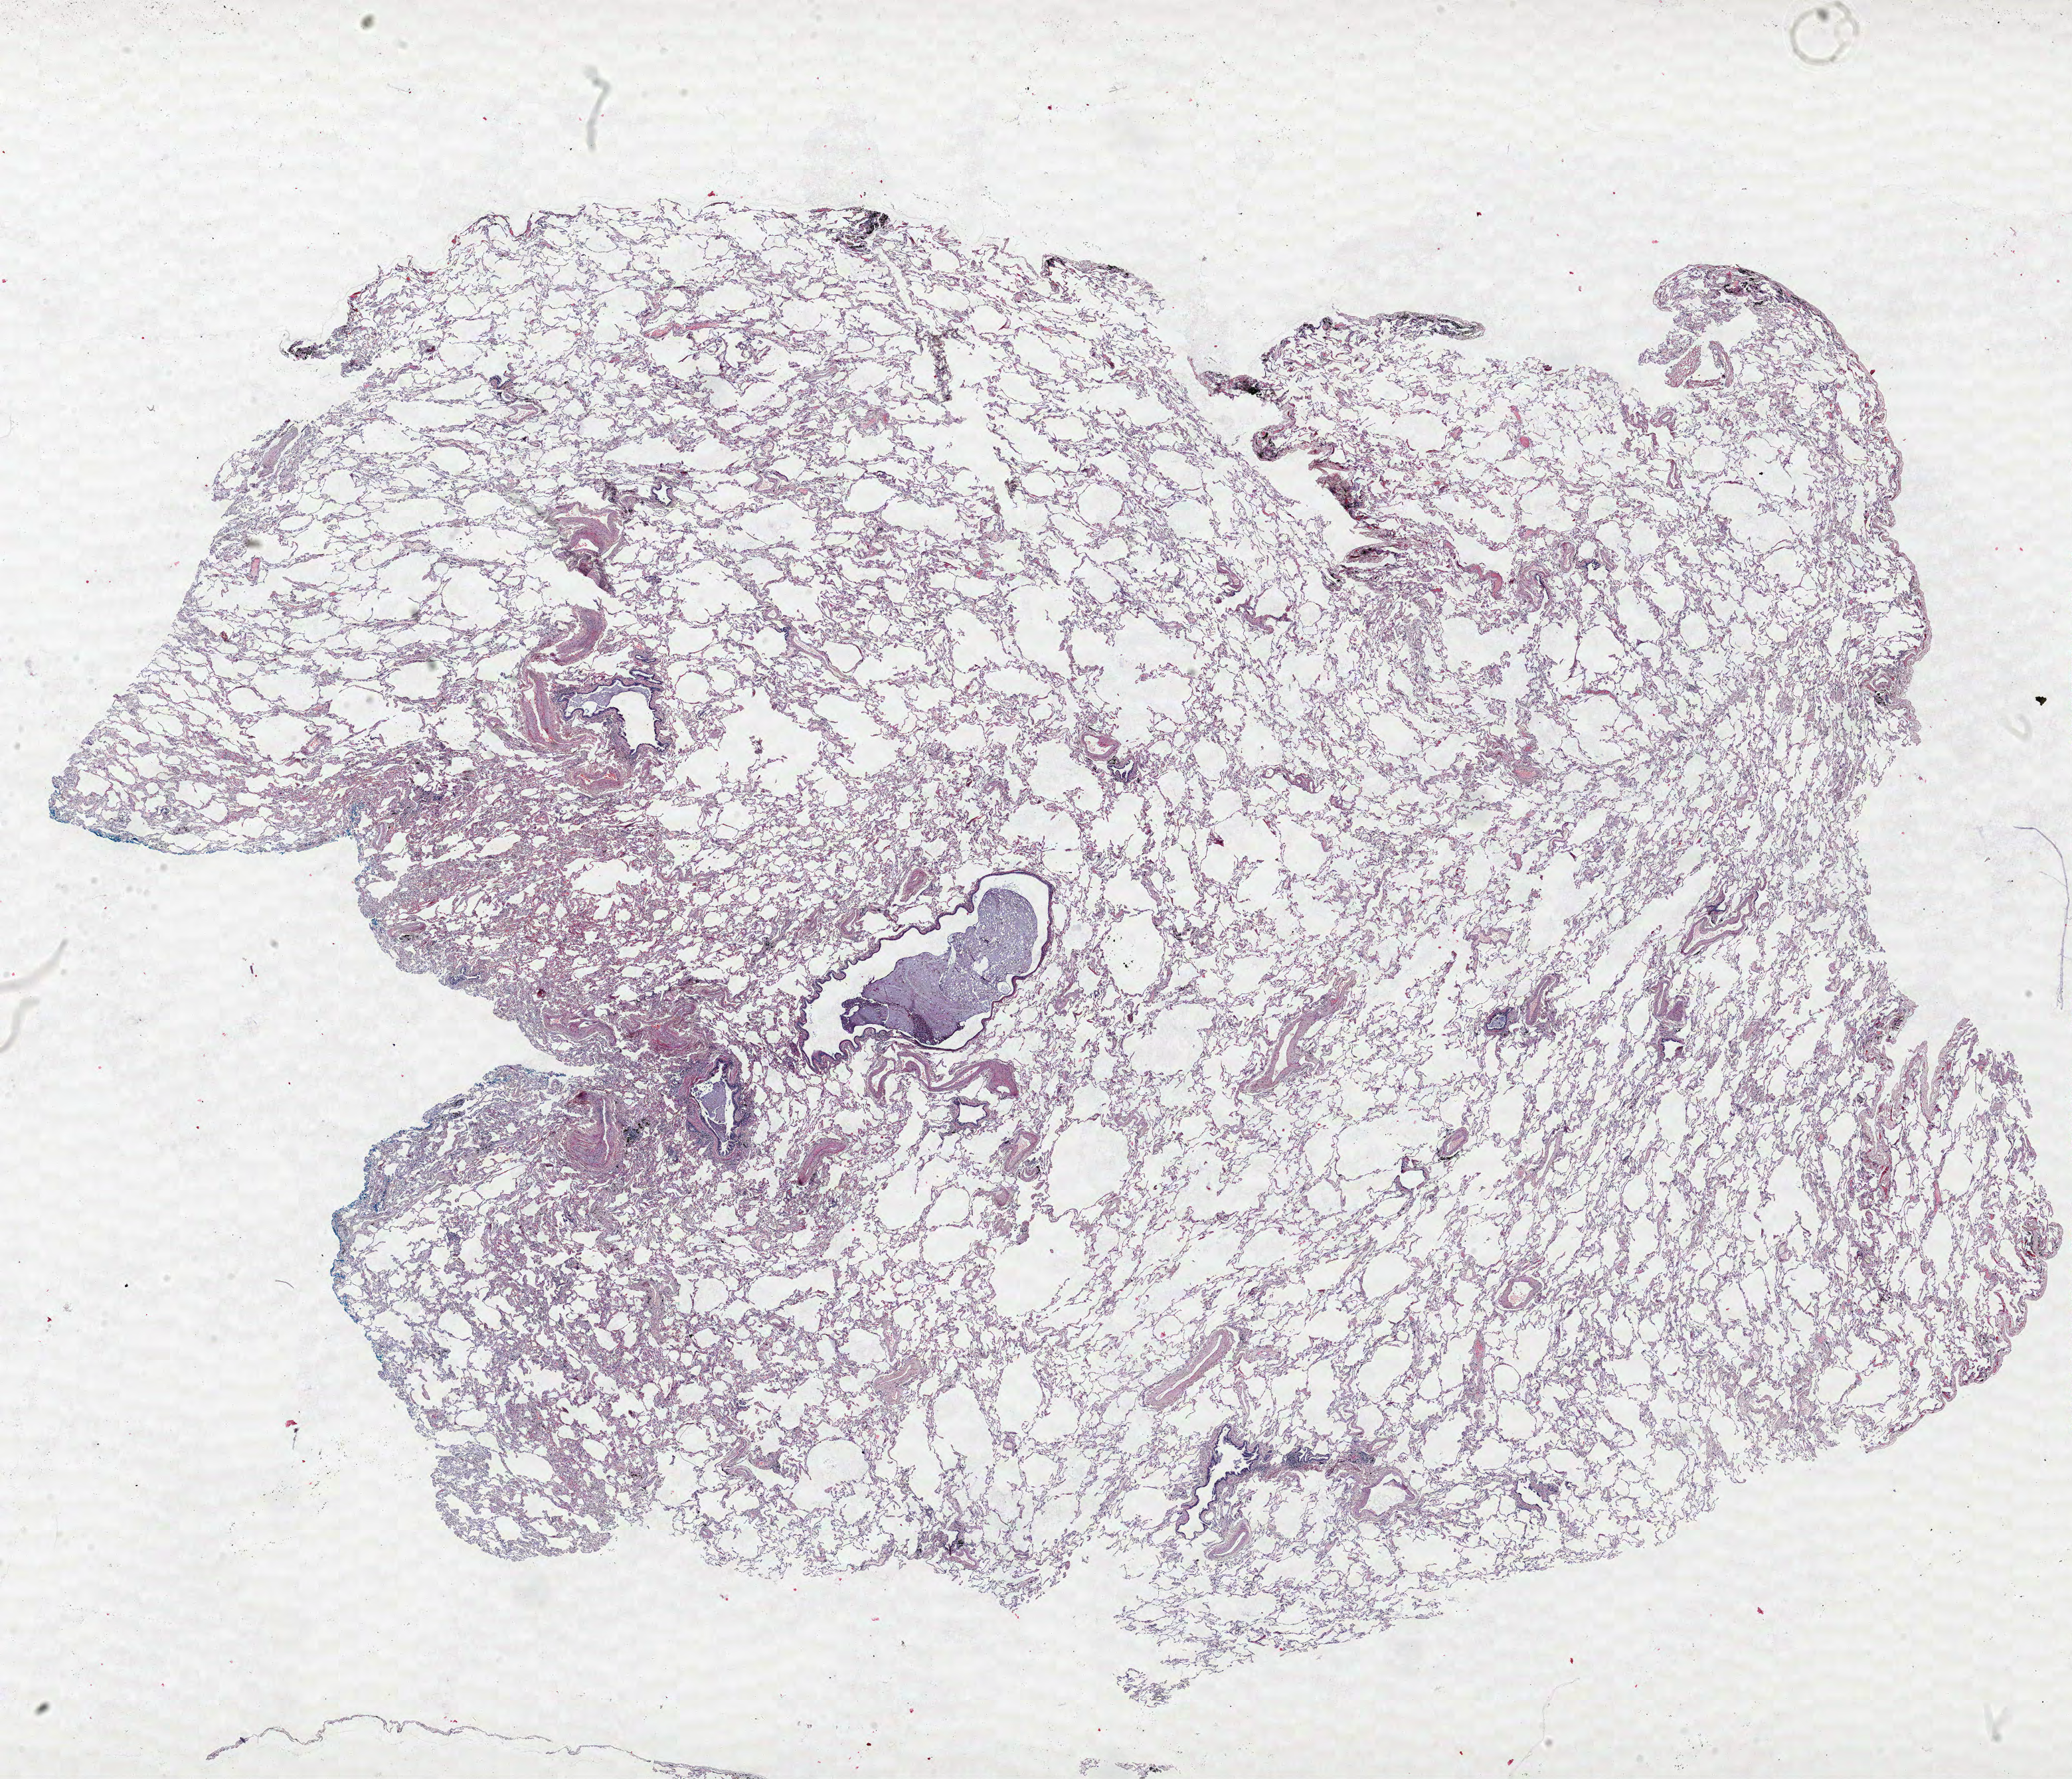
Whole-slide histology image, H&E-stained, a low-resolution overview of the entire scanned area, about 25.0 x 21.4 mm, formalin-fixed paraffin-embedded (FFPE) section, lung. Female patient, aged 72 at enrolment. Current smoker at enrolment. Grade: well differentiated (G1).
Participant's lung-cancer diagnosis: Bronchiolo-alveolar adenocarcinoma, NOS (ICD-O-3 8250/3). Tumour size (pathology): 23 mm. Stage (AJCC 6th edition): IA. Primary tumour location (clinical record): right upper lobe.